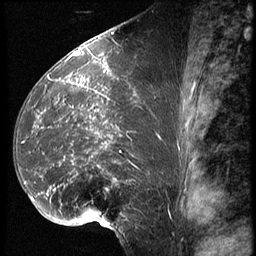
Breast MRI (dynamic contrast-enhanced), one sagittal slice. Position 33 of 62 along the scan axis. 3 images stored at this slice position (order not interpretable as contrast timing). 1.5 T. TE 4.2 ms, TR 9 ms. 2.5 mm slice thickness. 256 × 256 image matrix. Female patient, age 39 years. Case-level facts recorded for this patient, not image findings: setting: breast cancer imaged before/during neoadjuvant chemotherapy; receptor status: HER2-positive.
Outlined on this slice (semi-automatically segmented with operator editing):
- analysis volume of interest (the breast-tissue region the enhancement analysis was run in; not a lesion): bounding box <16,64,164,228> (left, top, right, bottom; pixels)
- tumour enhancement mask (voxels above the 140 % enhancement threshold inside the analysis volume of interest): <35,78,161,222>